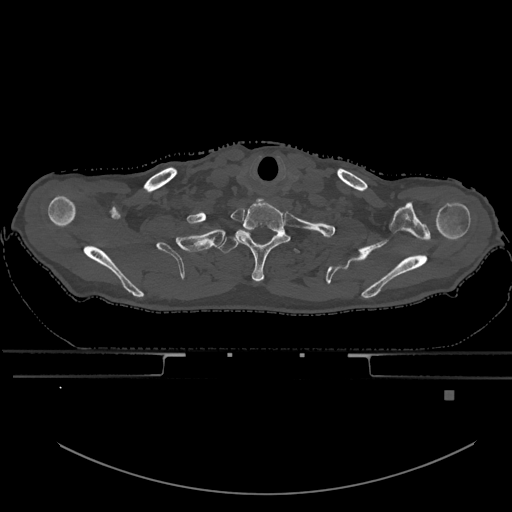
CT including the spine, one axial slice; position 566 of 969 along the scan axis; bone window (W 1800 / L 400 HU); 512 × 512 image matrix, field of view 456 × 456 mm. Patient: male, 82 years. Case-level facts recorded for this patient, not image findings: primary cancer: prostate.
Annotated regions visible in this slice (semi-automatically segmented with operator editing):
- T1 vertebra: bounding box [x1, y1, x2, y2] px = [218, 237, 300, 255]